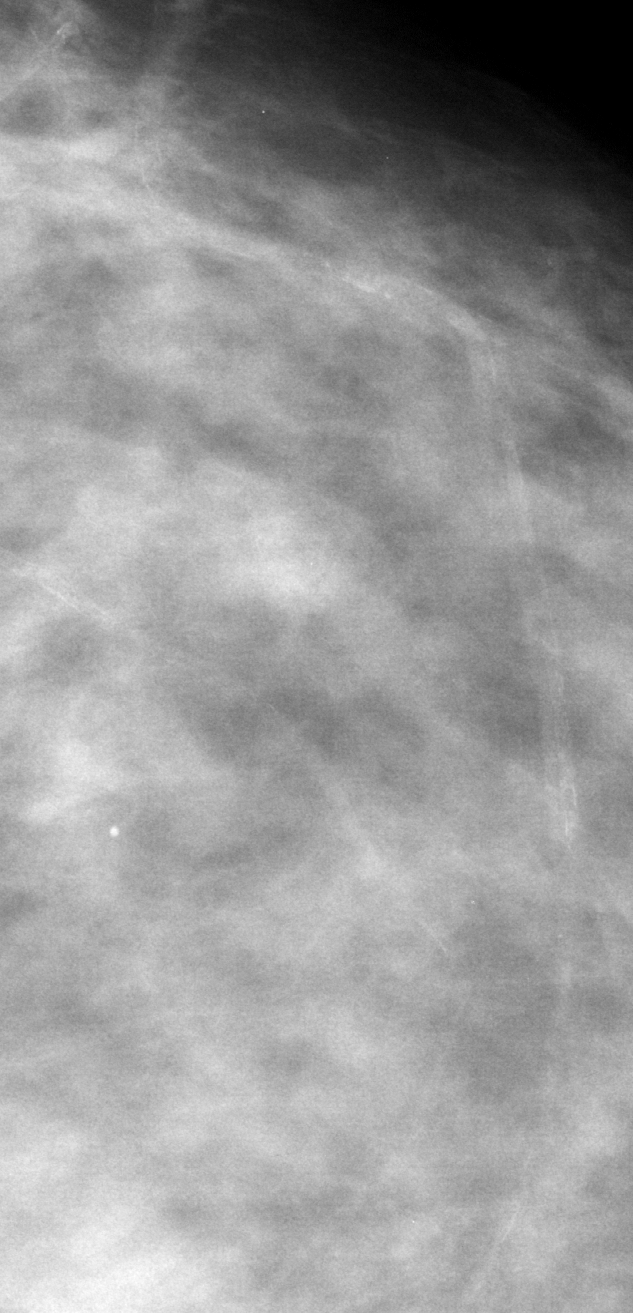
Cropped region of a digitized screen-film mammogram centred on a radiologist-marked abnormality; left breast; CC view; BI-RADS breast density category 2 (scale 1–4).
Marked abnormality: calcifications, morphology vascular; BI-RADS assessment category 2; subtlety rating 4 on a 1 (subtle) to 5 (obvious) scale; benign; no additional work-up was recommended (benign without callback).